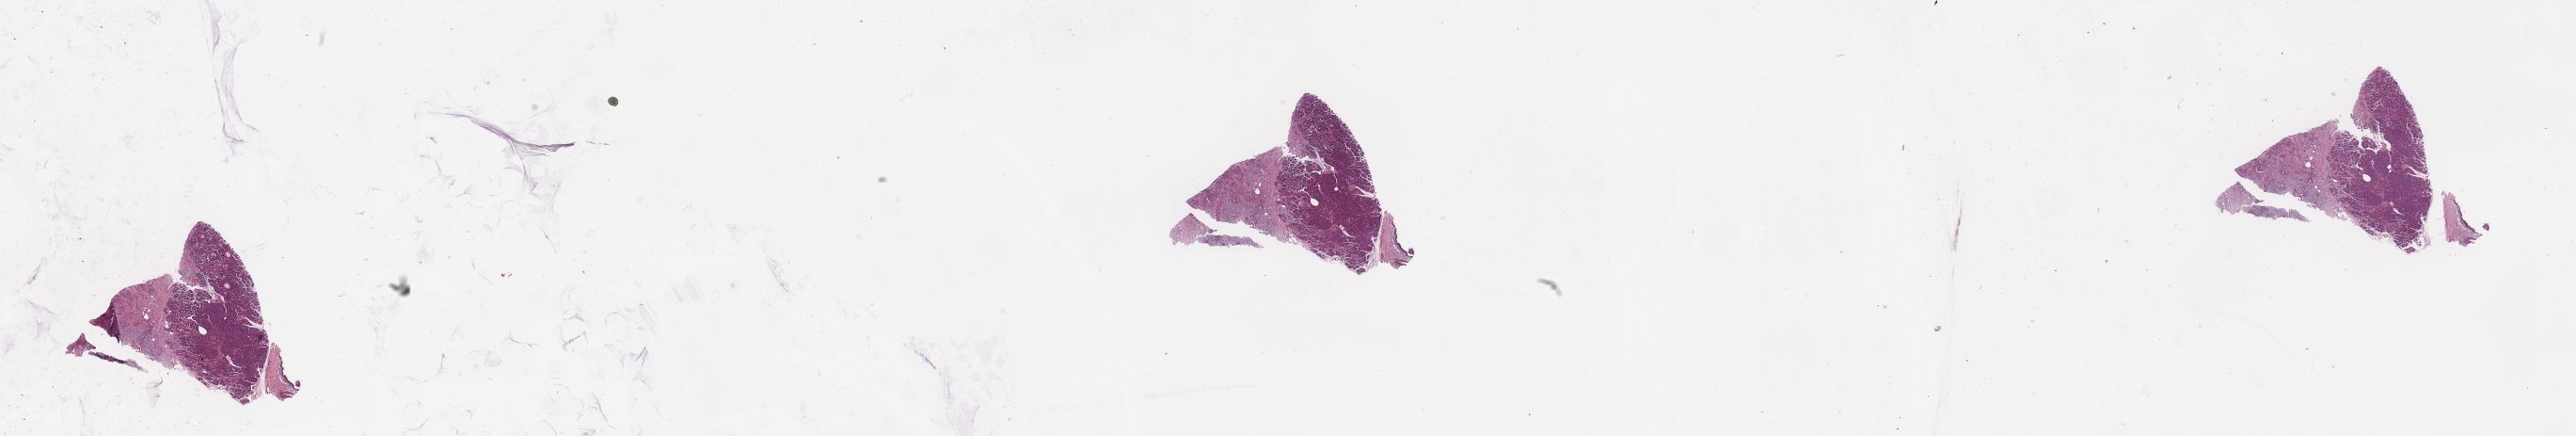
H&E-stained whole-slide image, low-resolution overview of the scanned area, about 43.3 x 7.3 mm (slide scanned at 20x), tumour tissue sample, pancreas. 70-year-old female patient.
• patient diagnosis (cohort enrolment): ductal adenocarcinoma (pancreas)
• primary tumour site (as recorded): head